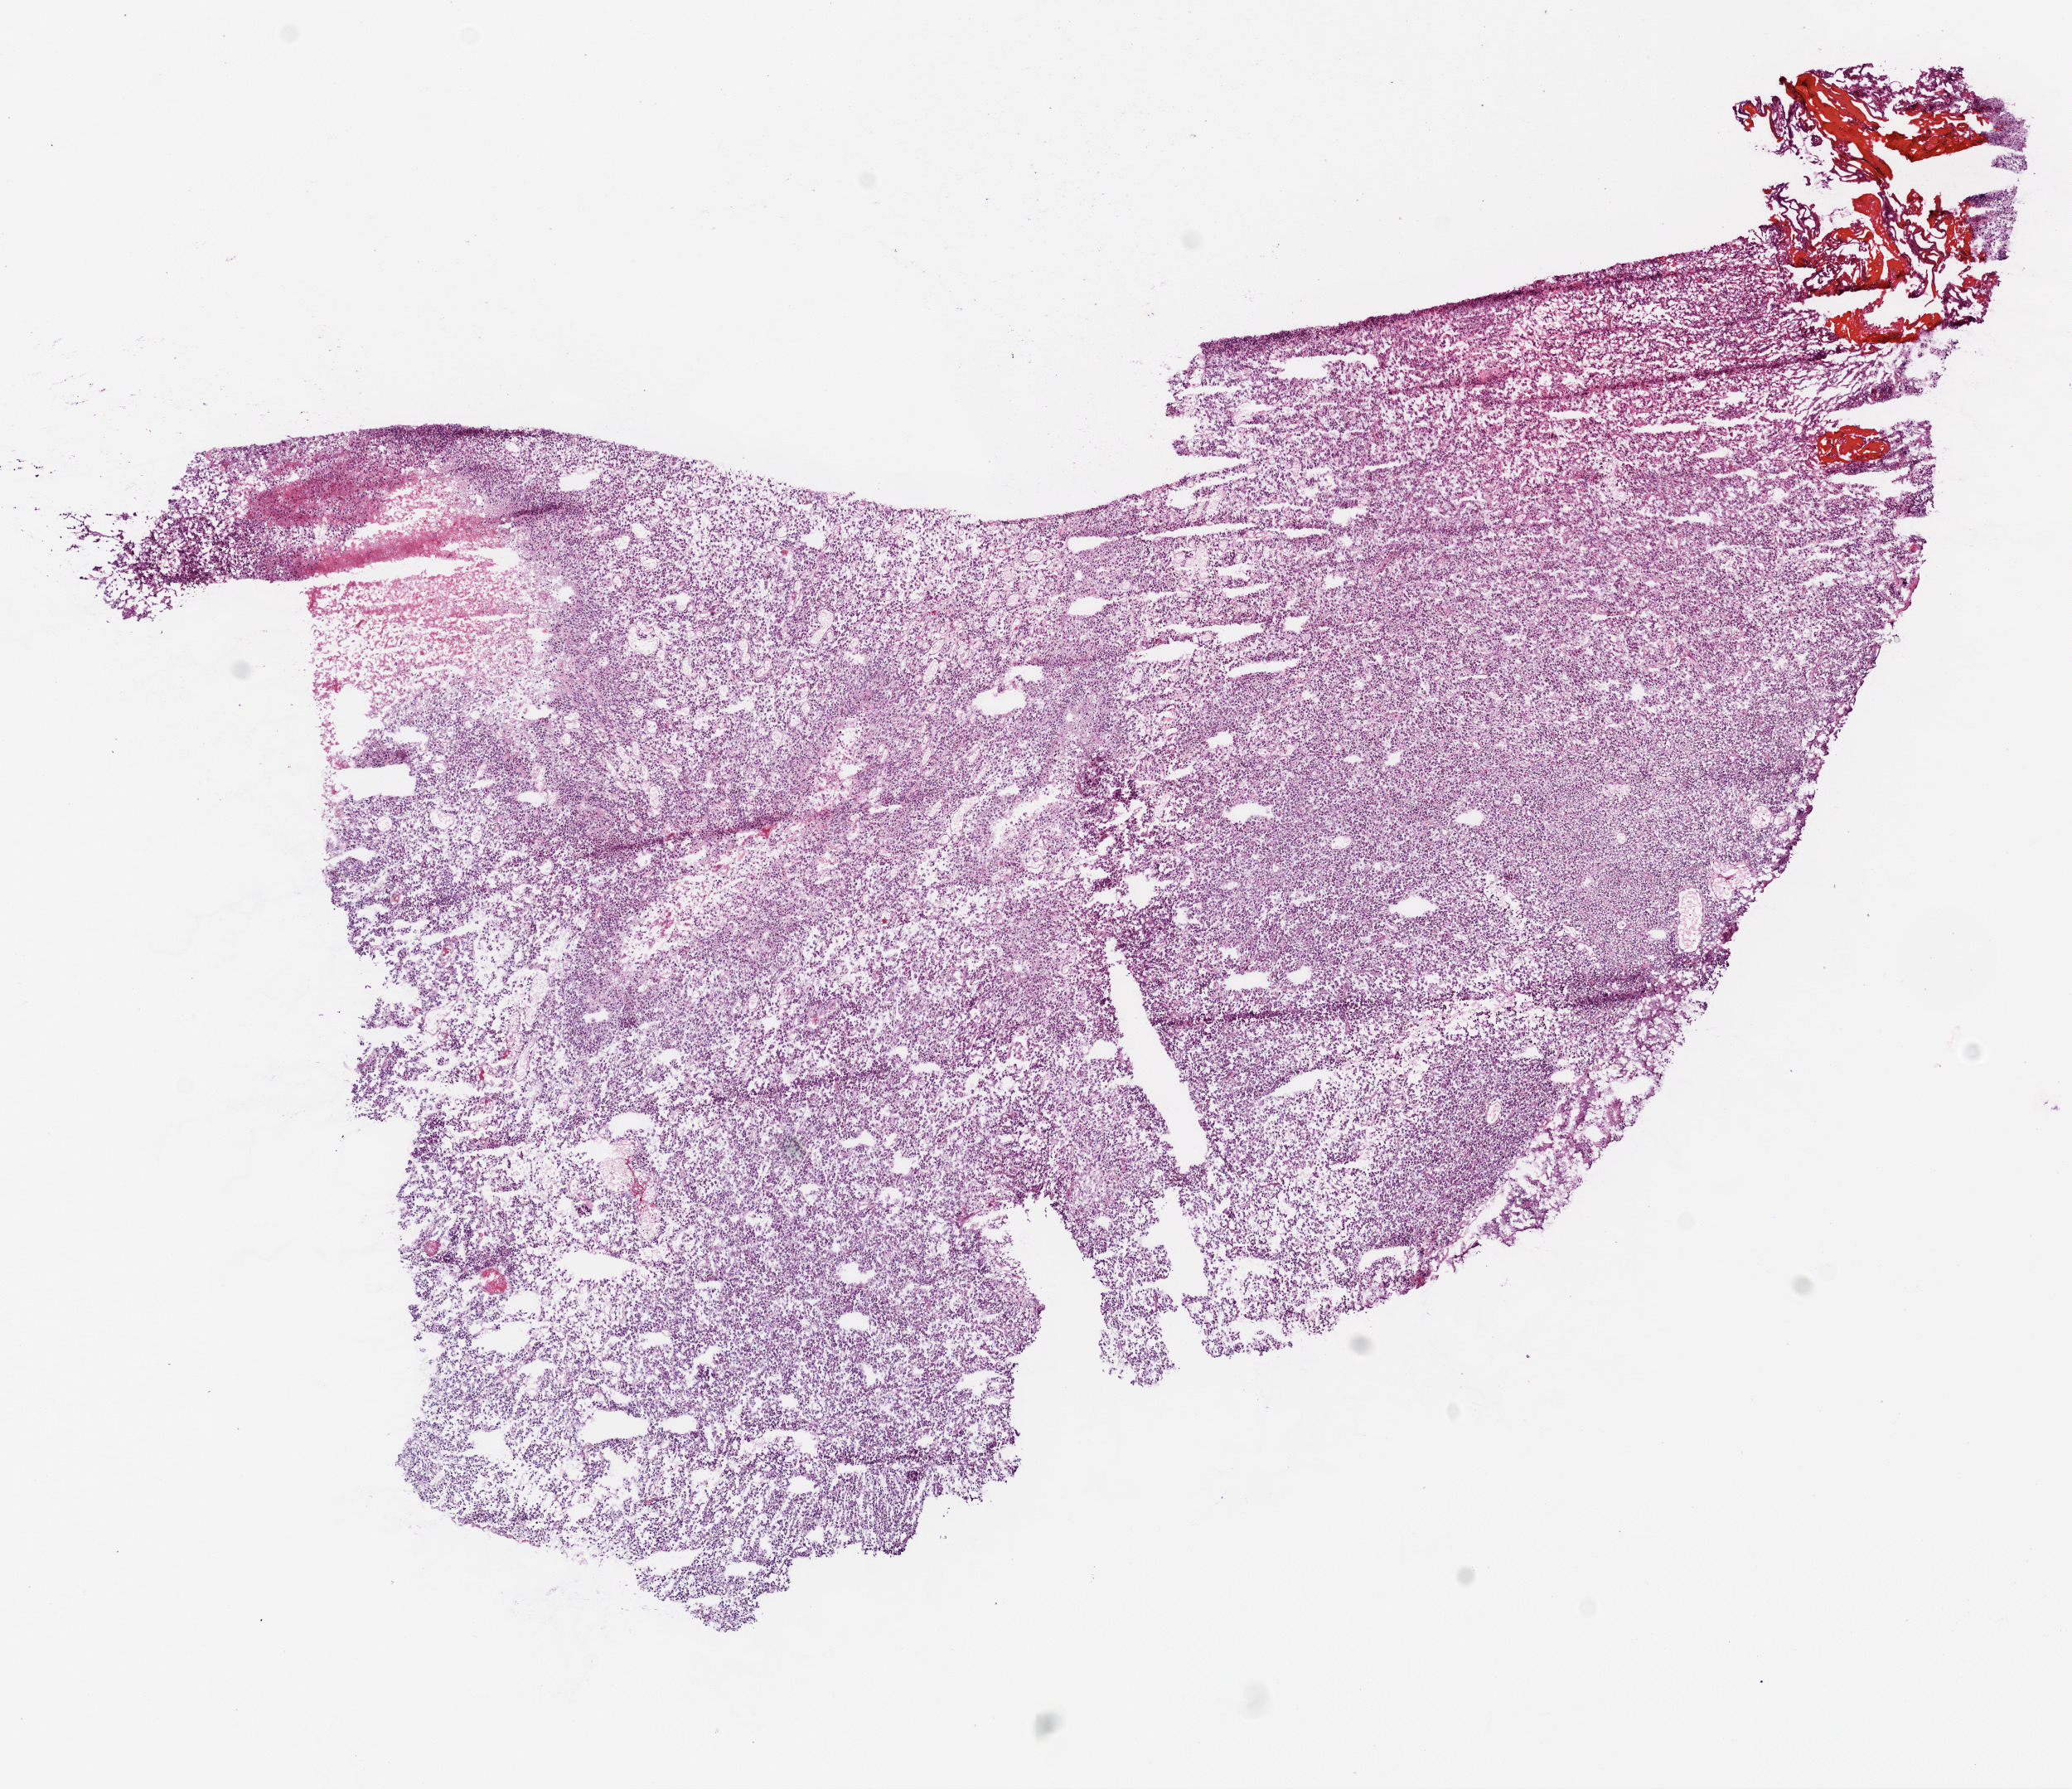
Digitized H&E tissue section (whole slide), whole scanned area (about 10.0 x 8.7 mm, acquisition: 20x scan) shown as a low-resolution overview; frozen section from the bottom of the tissue portion; brain, primary tumour sample. Male patient; age at initial diagnosis 57 years. Slide review estimates, as recorded: tumour cells 90%, tumour nuclei 95%, normal cells 0%, stromal cells 0%, necrosis 10%.
Pathologic diagnosis: Glioblastoma.